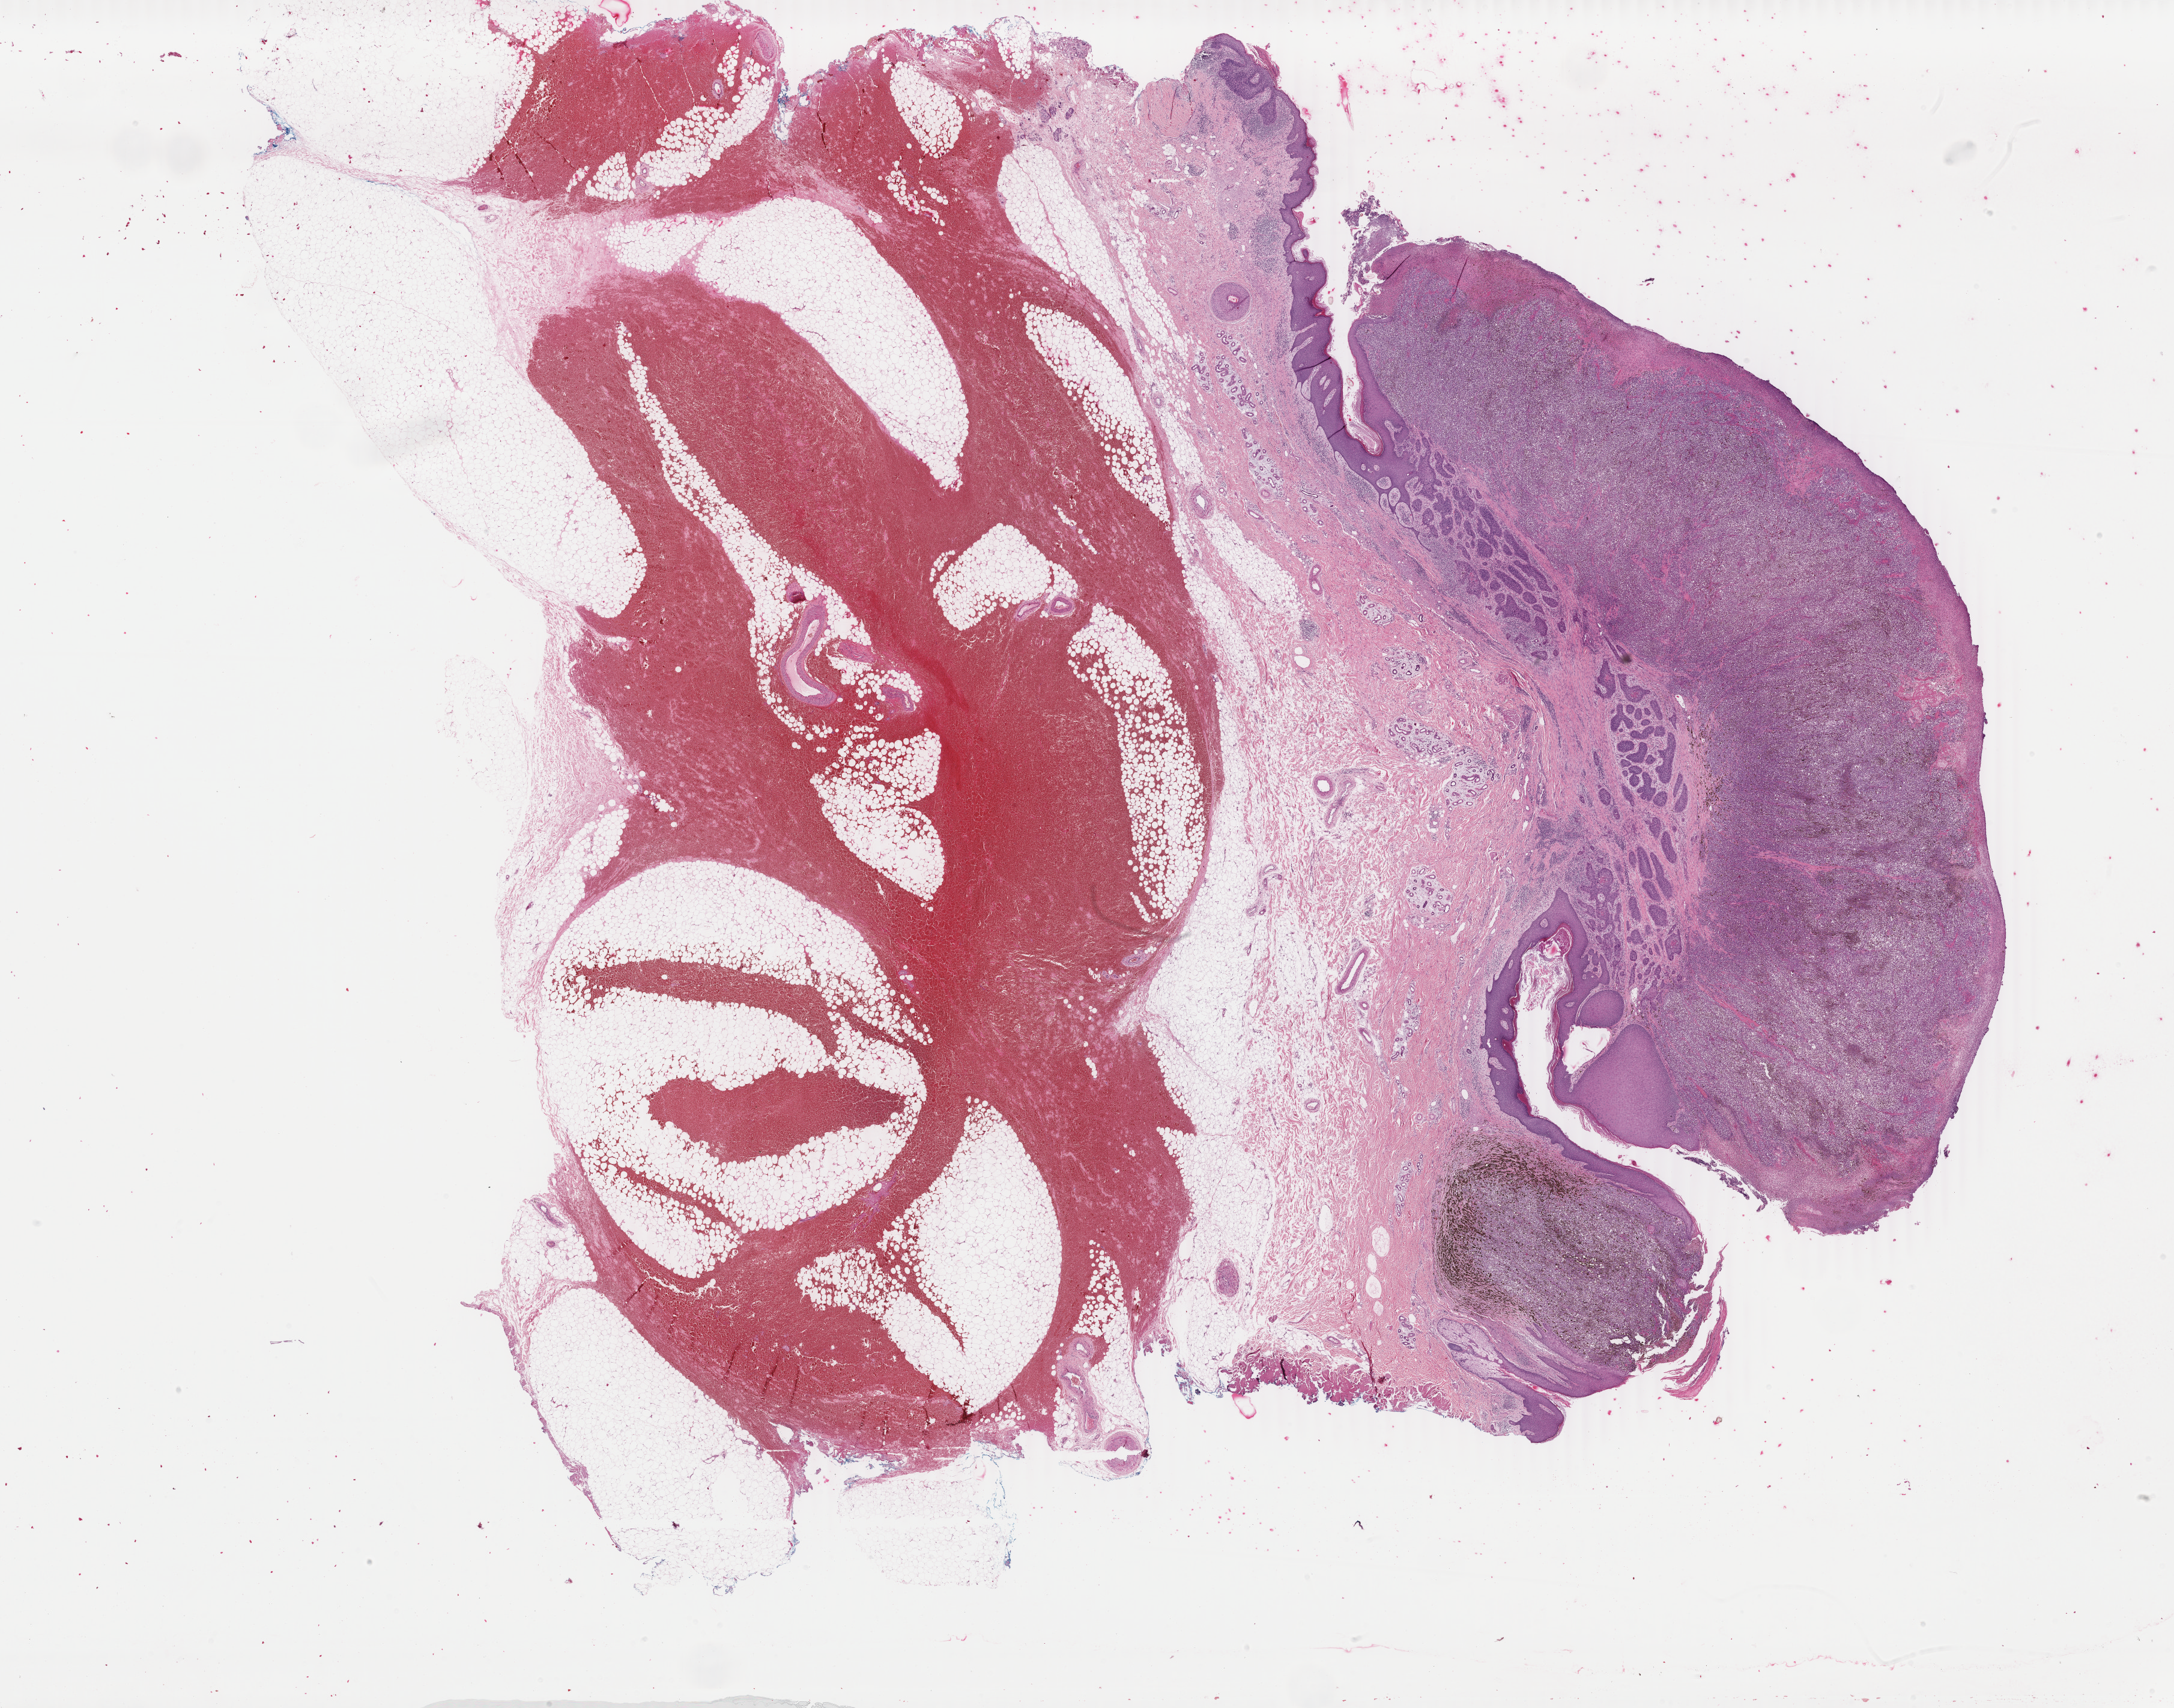
Whole-slide histology image, Hematoxylin and eosin (H&E) stained — whole scanned area (about 28.8 x 22.6 mm) shown as a low-resolution overview; FFPE section; primary tumour sample from the skin. Male, age 85 years at initial diagnosis.
* pathologic diagnosis: Malignant melanoma, NOS